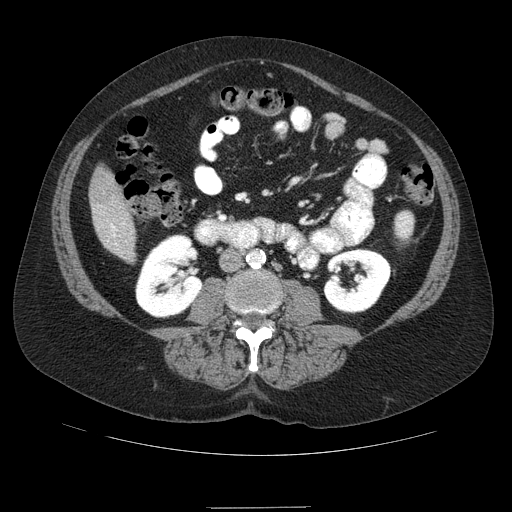
Contrast-enhanced abdominal CT (liver protocol), one axial slice. Slice 17 of 89 in the series (ordered by position). Reconstruction kernel STANDARD. Soft-tissue window (W 400 / L 40 HU). 512 × 512 image matrix. Case-level facts recorded for this patient, not image findings: diagnosis: hepatocellular carcinoma (patient treated with transarterial chemoembolisation; whether this scan precedes or follows treatment is not stated here); TNM stage (as recorded): Stage-IIIB; Child-Pugh class: A.
Outlined on this slice (semi-automatic segmentation, software-assisted and operator-edited):
- liver parenchyma outside the tumour (the mass and vessels are separate outlines, so this box may not span the whole liver): bounding box [x1, y1, x2, y2] px = [89, 166, 136, 259]
- liver vessels: [110, 224, 117, 237]